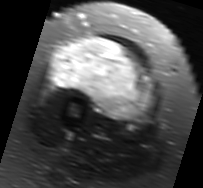
MRI of an extremity soft-tissue mass, one axial slice. T2-weighted fat-saturated. MR volume resampled by the dataset authors to the PET/CT grid (not the native acquisition matrix). 203 × 188 image matrix, field of view 198 × 184 mm. Female patient. From the clinical record (not read from this slice): histological type: malignant solitary fibrous tumor; grade: intermediate; site of the primary tumour: right thigh.
Outlined on this slice (expert contour drawn on MRI and transferred to this co-registered scan by the dataset authors):
- gross tumour volume including surrounding oedema: bounding box <49,37,157,123> (left, top, right, bottom; pixels)
- gross tumour volume (mass): <53,37,153,118>